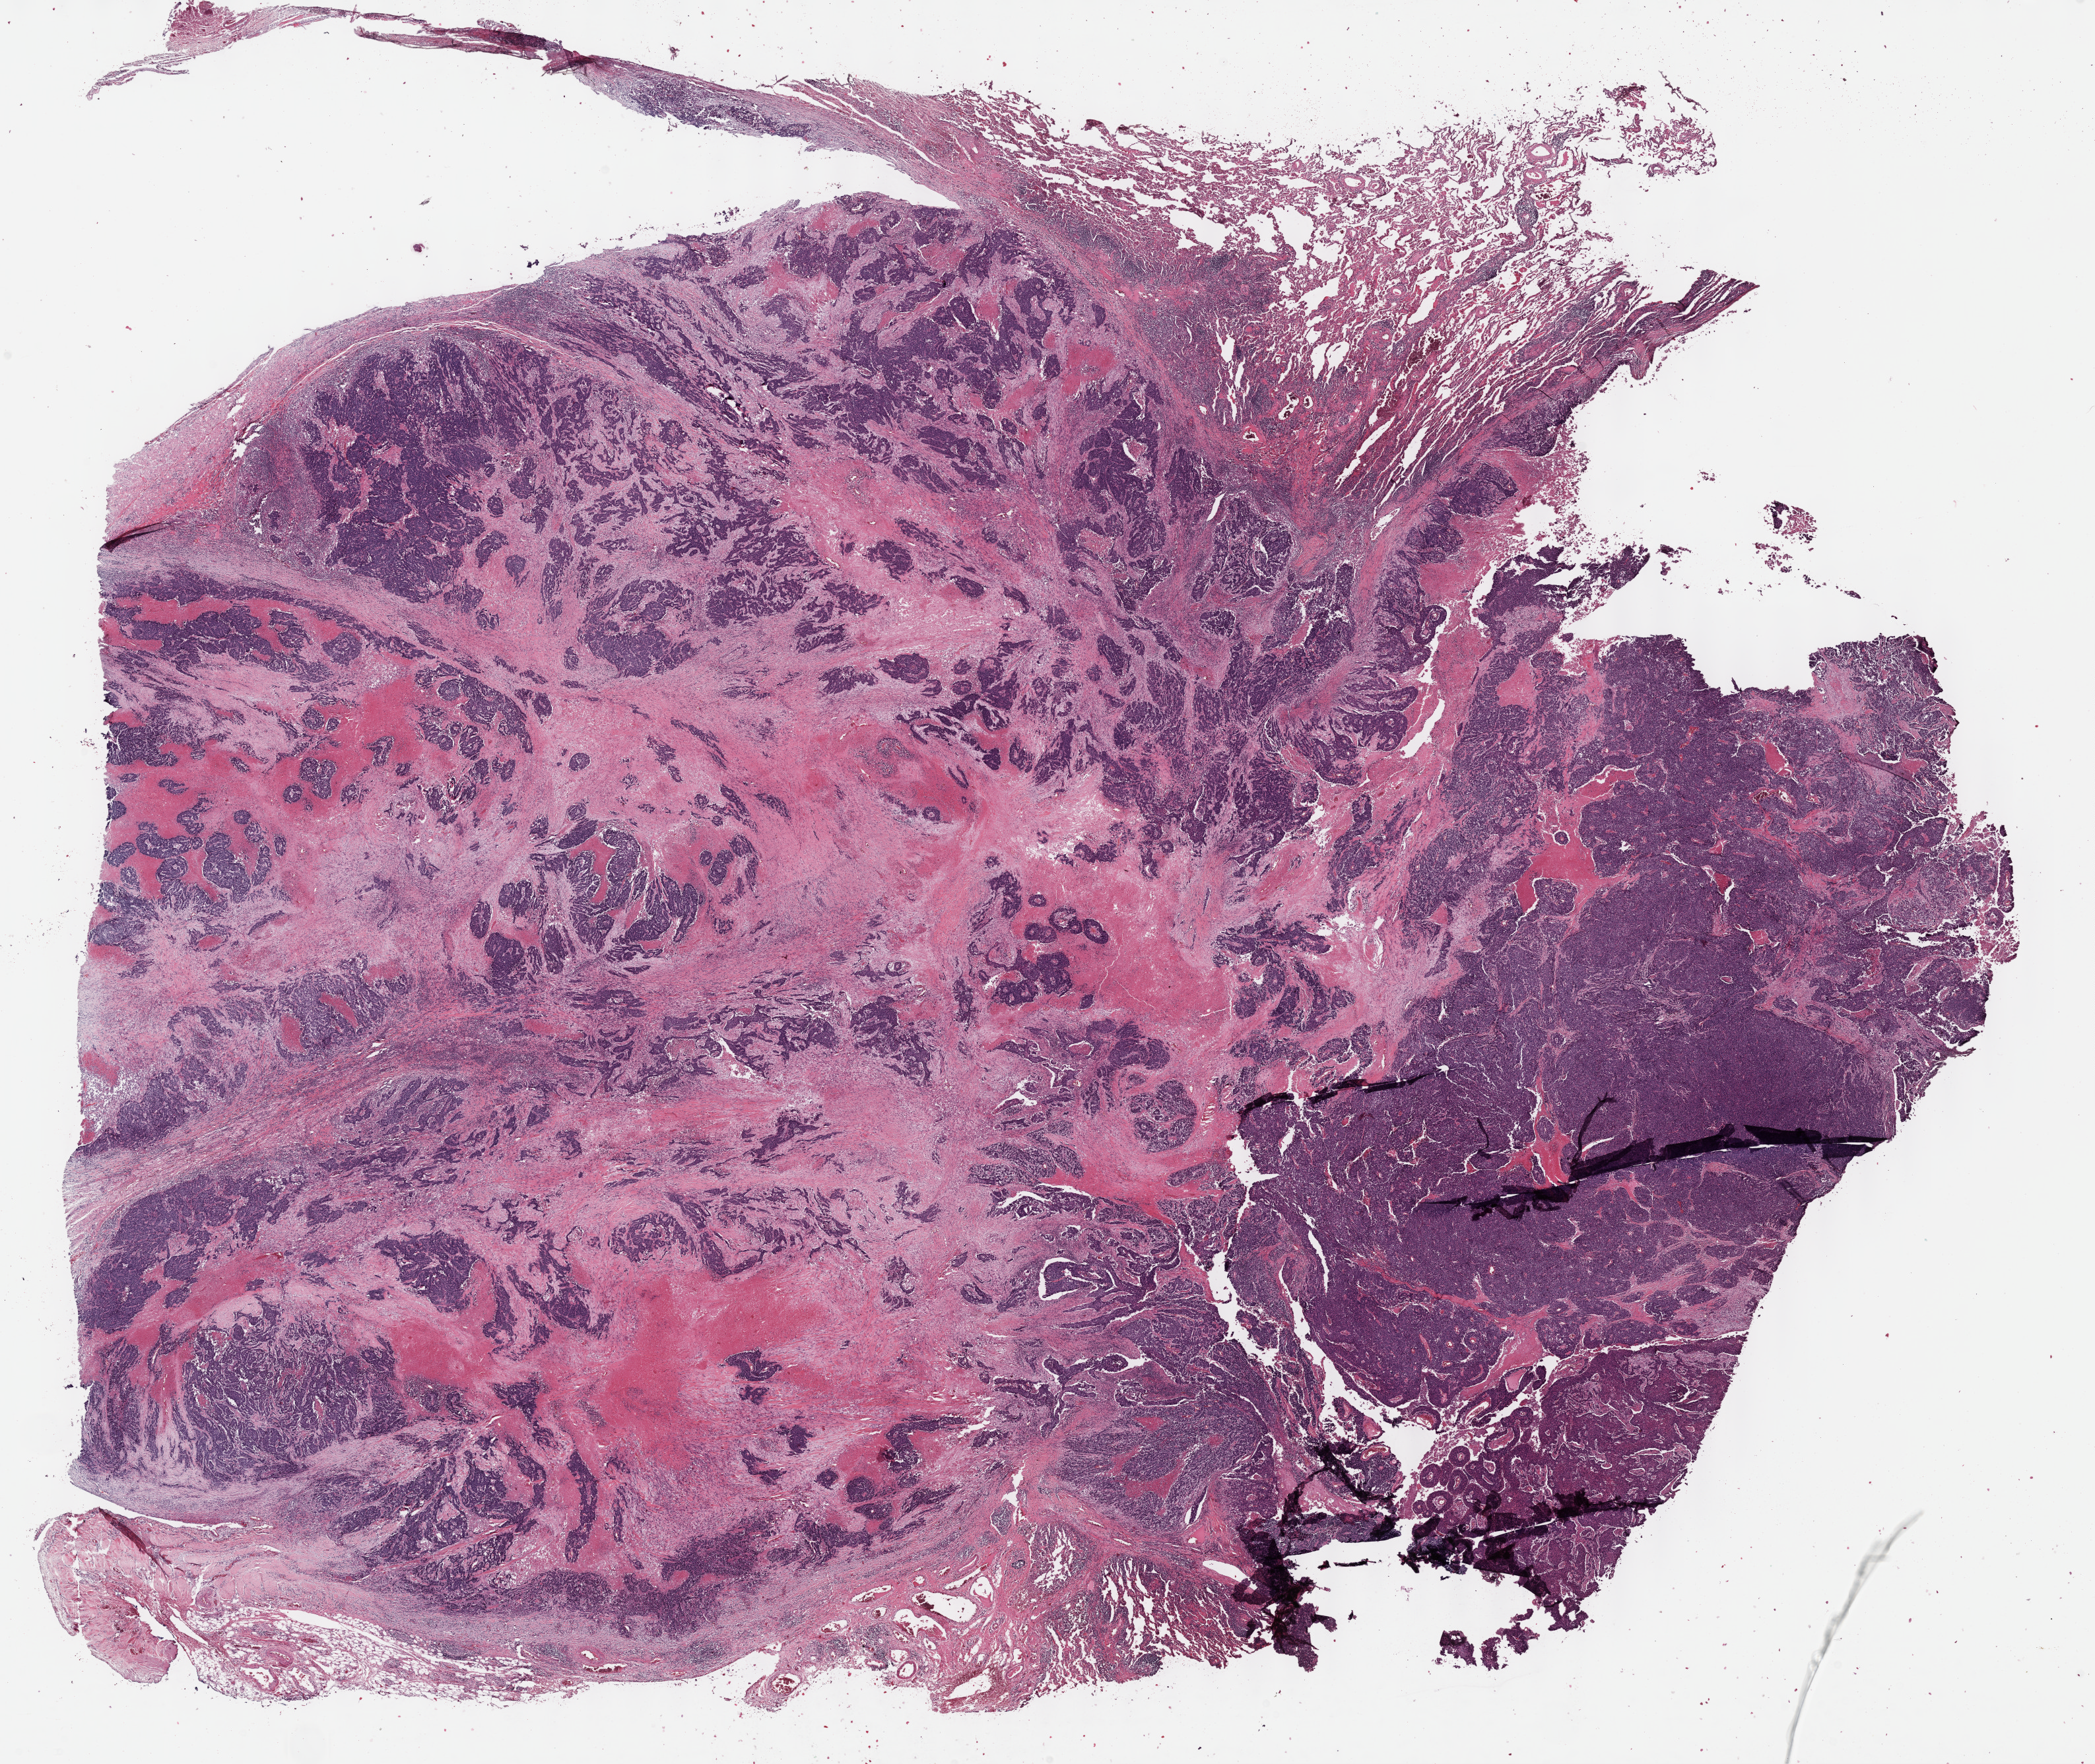
H&E whole-slide image, a low-resolution overview of the entire scanned area, about 25.7 x 21.6 mm (from a 40x scan), FFPE section, sample: primary tumour, lung. Female patient; age at initial diagnosis 57 years.
AJCC pathologic stage: III. Histologic diagnosis: Squamous cell carcinoma, NOS.